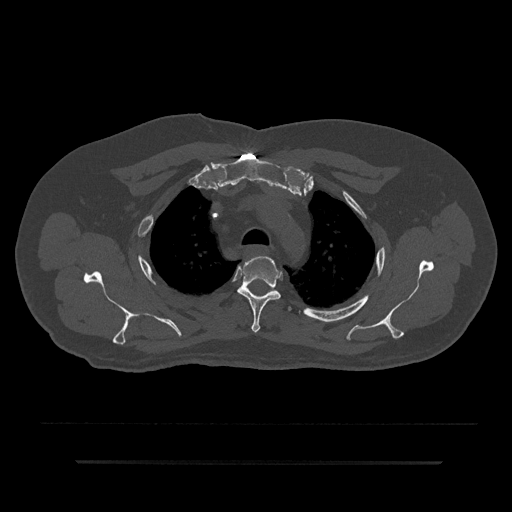
CT including the spine, one axial slice; 120 kVp; bone window (W 1800 / L 400 HU); 512 × 512 image matrix, field of view 464 × 464 mm. Patient: male, 59 years. From the clinical record (not read from this slice): primary cancer: bile ducts; vertebrae with lytic lesions (as recorded): T10.
Structures marked on this image (semi-automatic segmentation, software-assisted and operator-edited):
- T3 vertebra: bounding box (x1, y1, x2, y2) in pixels: (237, 256, 281, 333)
- T4 vertebra: (288, 306, 292, 311)